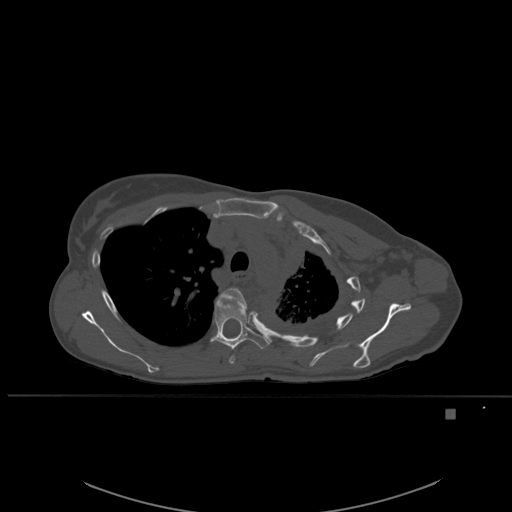
CT including the spine, one axial slice; slice 402 of 537 in the series (ordered by position); bone window (W 1800 / L 400 HU); 1.5 mm slice thickness; 512 × 512 image matrix, field of view 440 × 440 mm. Female patient, age 45 years. Case-level facts recorded for this patient, not image findings: primary cancer: lung.
Outlined on this slice (semi-automatic segmentation, software-assisted and operator-edited):
- T4 vertebra: box from (x=220, y=288) to (x=248, y=364) px
- T5 vertebra: (x=210, y=296)–(x=270, y=350)